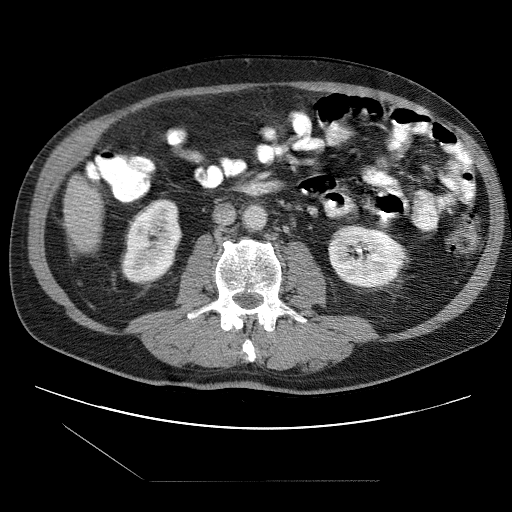
Contrast-enhanced abdominal CT (liver protocol), one axial slice; slice 12 of 109 in the series (ordered by position); reconstruction kernel STANDARD; one of 2 acquisitions stored at this slice position; soft-tissue window (W 400 / L 40 HU); 2.5 mm slice thickness; 512 × 512 image matrix. From the clinical record (not read from this slice): diagnosis: hepatocellular carcinoma (patient treated with transarterial chemoembolisation; whether this scan precedes or follows treatment is not stated here); TNM stage (as recorded): Stage-IIIB; Child-Pugh class: A.
Annotated regions visible in this slice (semi-automatically segmented with operator editing):
- liver parenchyma outside the tumour (the mass and vessels are separate outlines, so this box may not span the whole liver): box from (x=64, y=178) to (x=104, y=252) px